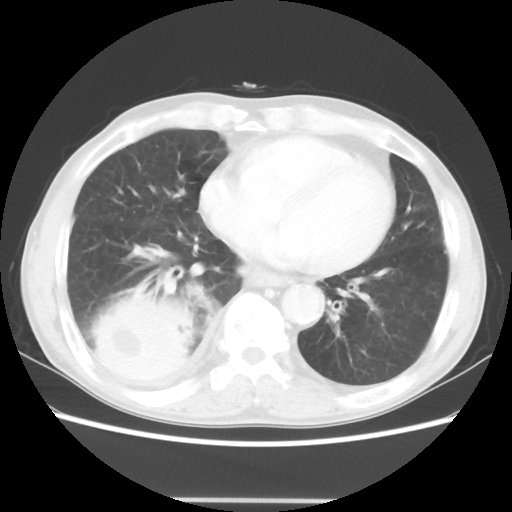
Chest CT, one axial slice. Slice 15 of 48 in the series (ordered by position). Lung window (W 1500 / L -600 HU). 5 mm slice thickness. 512 × 512 image matrix, field of view 361 × 361 mm. Patient: male, 66 years. Case-level facts recorded for this patient, not image findings: clinical TNM (as recorded): T4 N1 M1; histopathological grade: G3.
Outlined on this slice (rectangle marked by the reading radiologist):
- lung tumour (recorded histology: small cell carcinoma): bounding box <70,286,202,390> (left, top, right, bottom; pixels)